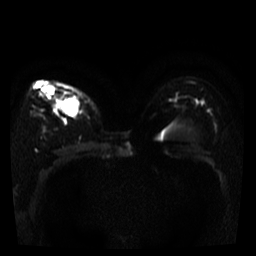
Breast MRI, one axial slice. Position 25 of 39 along the scan axis. Diffusion-weighted series; image 2 of 4 stored at this slice position (different b-values; order by instance number). 3 T. 256 × 256 image matrix, field of view 280 × 280 mm. Female patient.
Outlined on this slice (manually delineated by an expert):
- tumour on diffusion-weighted imaging: bounding box <61,102,73,115> (left, top, right, bottom; pixels)